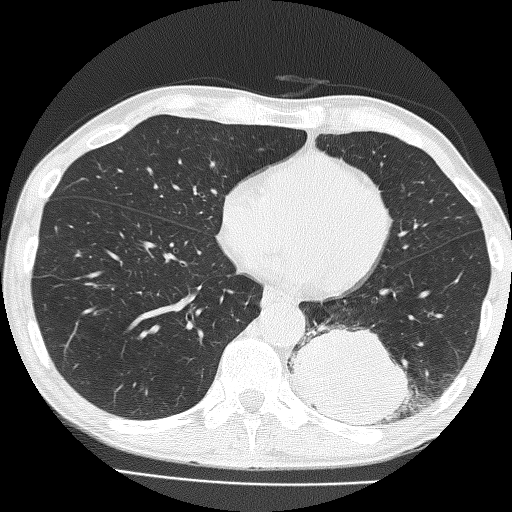
Axial slice from a low-dose chest CT screening exam. Baseline annual screen. Lung window (W 1500 / L -600 HU). Lung (sharp) reconstruction kernel (FC51). 120 kVp. Slice 99 of 160 in the series. 512 × 512 image matrix, field of view 324 × 324 mm. Male participant, aged 58 years at enrolment.
Expert reader's lesion annotation, bounding box (x1, y1, x2, y2) in pixels: (295, 302, 425, 434). The screening reader recorded 2 non-calcified nodules or masses ≥4 mm on this exam (left lower lobe, left upper lobe); which of them this box marks is not recorded. Official screen result: positive, change unspecified: nodule(s) >= 4 mm or enlarging nodule(s), mass(es), or other non-specific abnormalities suspicious for lung cancer. Later outcome: lung cancer diagnosed 39 days after this screen — non-small cell carcinoma, left lower lobe, poorly differentiated (G3), stage IV (AJCC 6th edition), 74 mm at pathology.